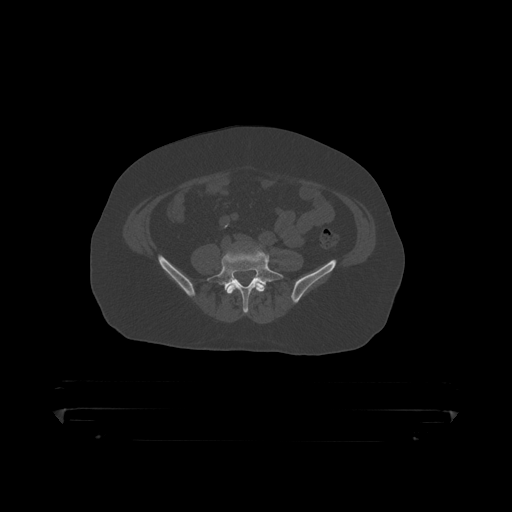
CT including the spine, one axial slice; position 45 of 390 along the scan axis; reconstruction kernel STANDARD; bone window (W 1800 / L 400 HU); 1.25 mm slice thickness; 512 × 512 image matrix, field of view 650 × 650 mm. Patient: male, 60 years. From the clinical record (not read from this slice): primary cancer: prostate.
Annotated regions visible in this slice (semi-automatically segmented with operator editing):
- L4 vertebra: box from (x=227, y=281) to (x=265, y=295) px
- L5 vertebra: (x=208, y=252)–(x=284, y=313)